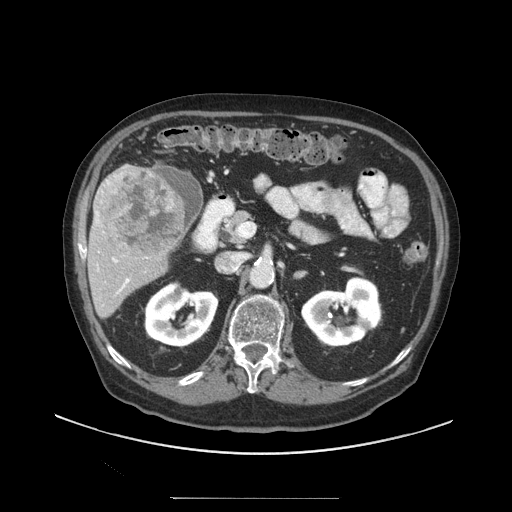
Contrast-enhanced abdominal CT (liver protocol), one axial slice. Position 47 of 97 along the scan axis. Reconstruction kernel STANDARD. 140 kVp. Soft-tissue window (W 400 / L 40 HU). 2.5 mm slice thickness. 512 × 512 image matrix, field of view 450 × 450 mm. Case-level facts recorded for this patient, not image findings: diagnosis: hepatocellular carcinoma (patient treated with transarterial chemoembolisation; whether this scan precedes or follows treatment is not stated here); TNM stage (as recorded): Stage-IIIC; Child-Pugh class: A; tumour differentiation: well differentiated; tumour nodularity: uninodular.
Annotated regions visible in this slice (semi-automatically segmented with operator editing):
- liver parenchyma outside the tumour (the mass and vessels are separate outlines, so this box may not span the whole liver): box from (x=88, y=164) to (x=202, y=318) px
- mass: (x=97, y=166)–(x=186, y=258)
- liver vessels: (x=95, y=219)–(x=130, y=293)